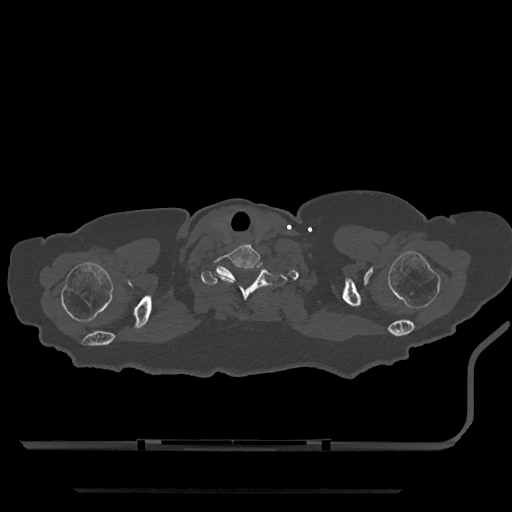
CT including the spine, one axial slice. Position 722 of 797 along the scan axis. Reconstruction kernel Br40s/3. 120 kVp. Bone window (W 1800 / L 400 HU). 0.5 mm slice thickness. 512 × 512 image matrix, field of view 440 × 440 mm. Patient: female, 51 years. Case-level facts recorded for this patient, not image findings: primary cancer: neuro; vertebrae with lytic lesions (as recorded): T8.
Structures marked on this image (semi-automatically segmented with operator editing):
- T1 vertebra: bounding box (x1, y1, x2, y2) in pixels: (201, 262, 288, 301)